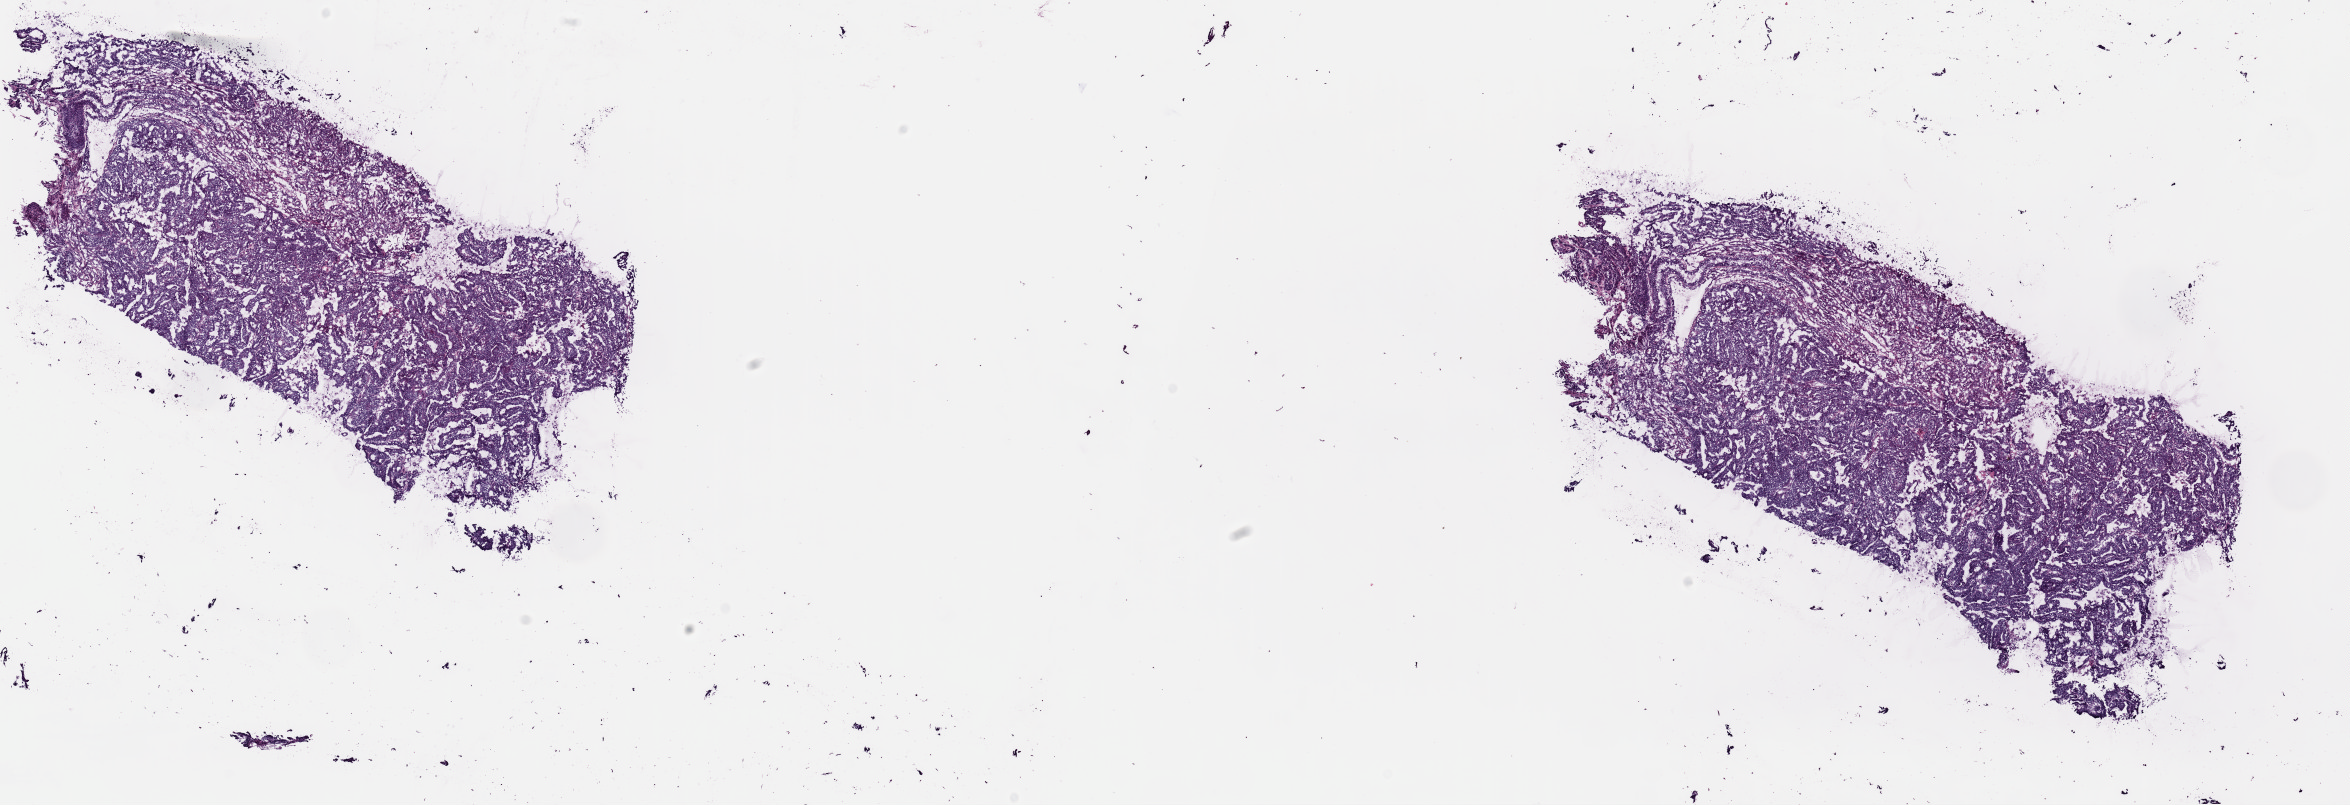
Digitized Hematoxylin and eosin (H&E) stained tissue section (whole slide) — shown as a low-resolution overview of the whole scanned area (about 18.6 x 6.4 mm, from a 40x scan), frozen section from the top of the tissue portion, uterus, primary tumour sample. Female, age 64 years at initial diagnosis. Histologic grade: G3 (poorly differentiated). Pathologist review of this section (percent, as recorded): tumour cells 94%, tumour nuclei 96%, normal cells 0%, stromal cells 5%, necrosis 1%. Inflammatory infiltration, as recorded: lymphocyte infiltration 1%, monocyte infiltration 0%, neutrophil infiltration 0%.
Diagnosis: Endometrioid adenocarcinoma, NOS (endometrium). FIGO stage: IB. Lymph nodes positive (case pathology): 0 of 22 examined.